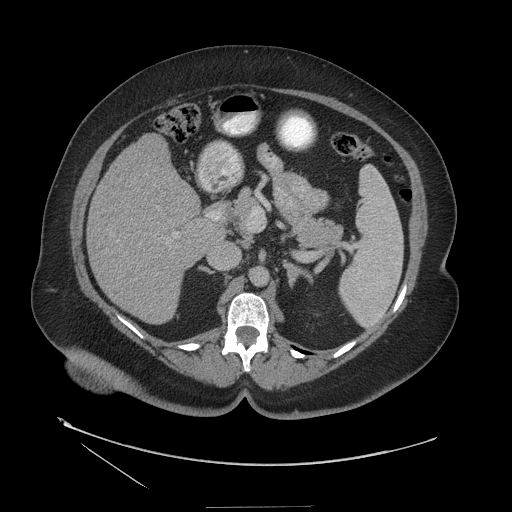
Contrast-enhanced abdominal CT (liver protocol), one axial slice. Position 65 of 127 along the scan axis. Reconstruction kernel STANDARD. 140 kVp. Soft-tissue window (W 400 / L 40 HU). 512 × 512 image matrix, field of view 480 × 480 mm. From the clinical record (not read from this slice): diagnosis: hepatocellular carcinoma (patient treated with transarterial chemoembolisation; whether this scan precedes or follows treatment is not stated here); TNM stage (as recorded): Stage-II; Child-Pugh class: A; tumour differentiation: well differentiated; tumour nodularity: multinodular.
Outlined on this slice (semi-automatic segmentation, software-assisted and operator-edited):
- liver parenchyma outside the tumour (the mass and vessels are separate outlines, so this box may not span the whole liver): box from (x=86, y=134) to (x=218, y=324) px